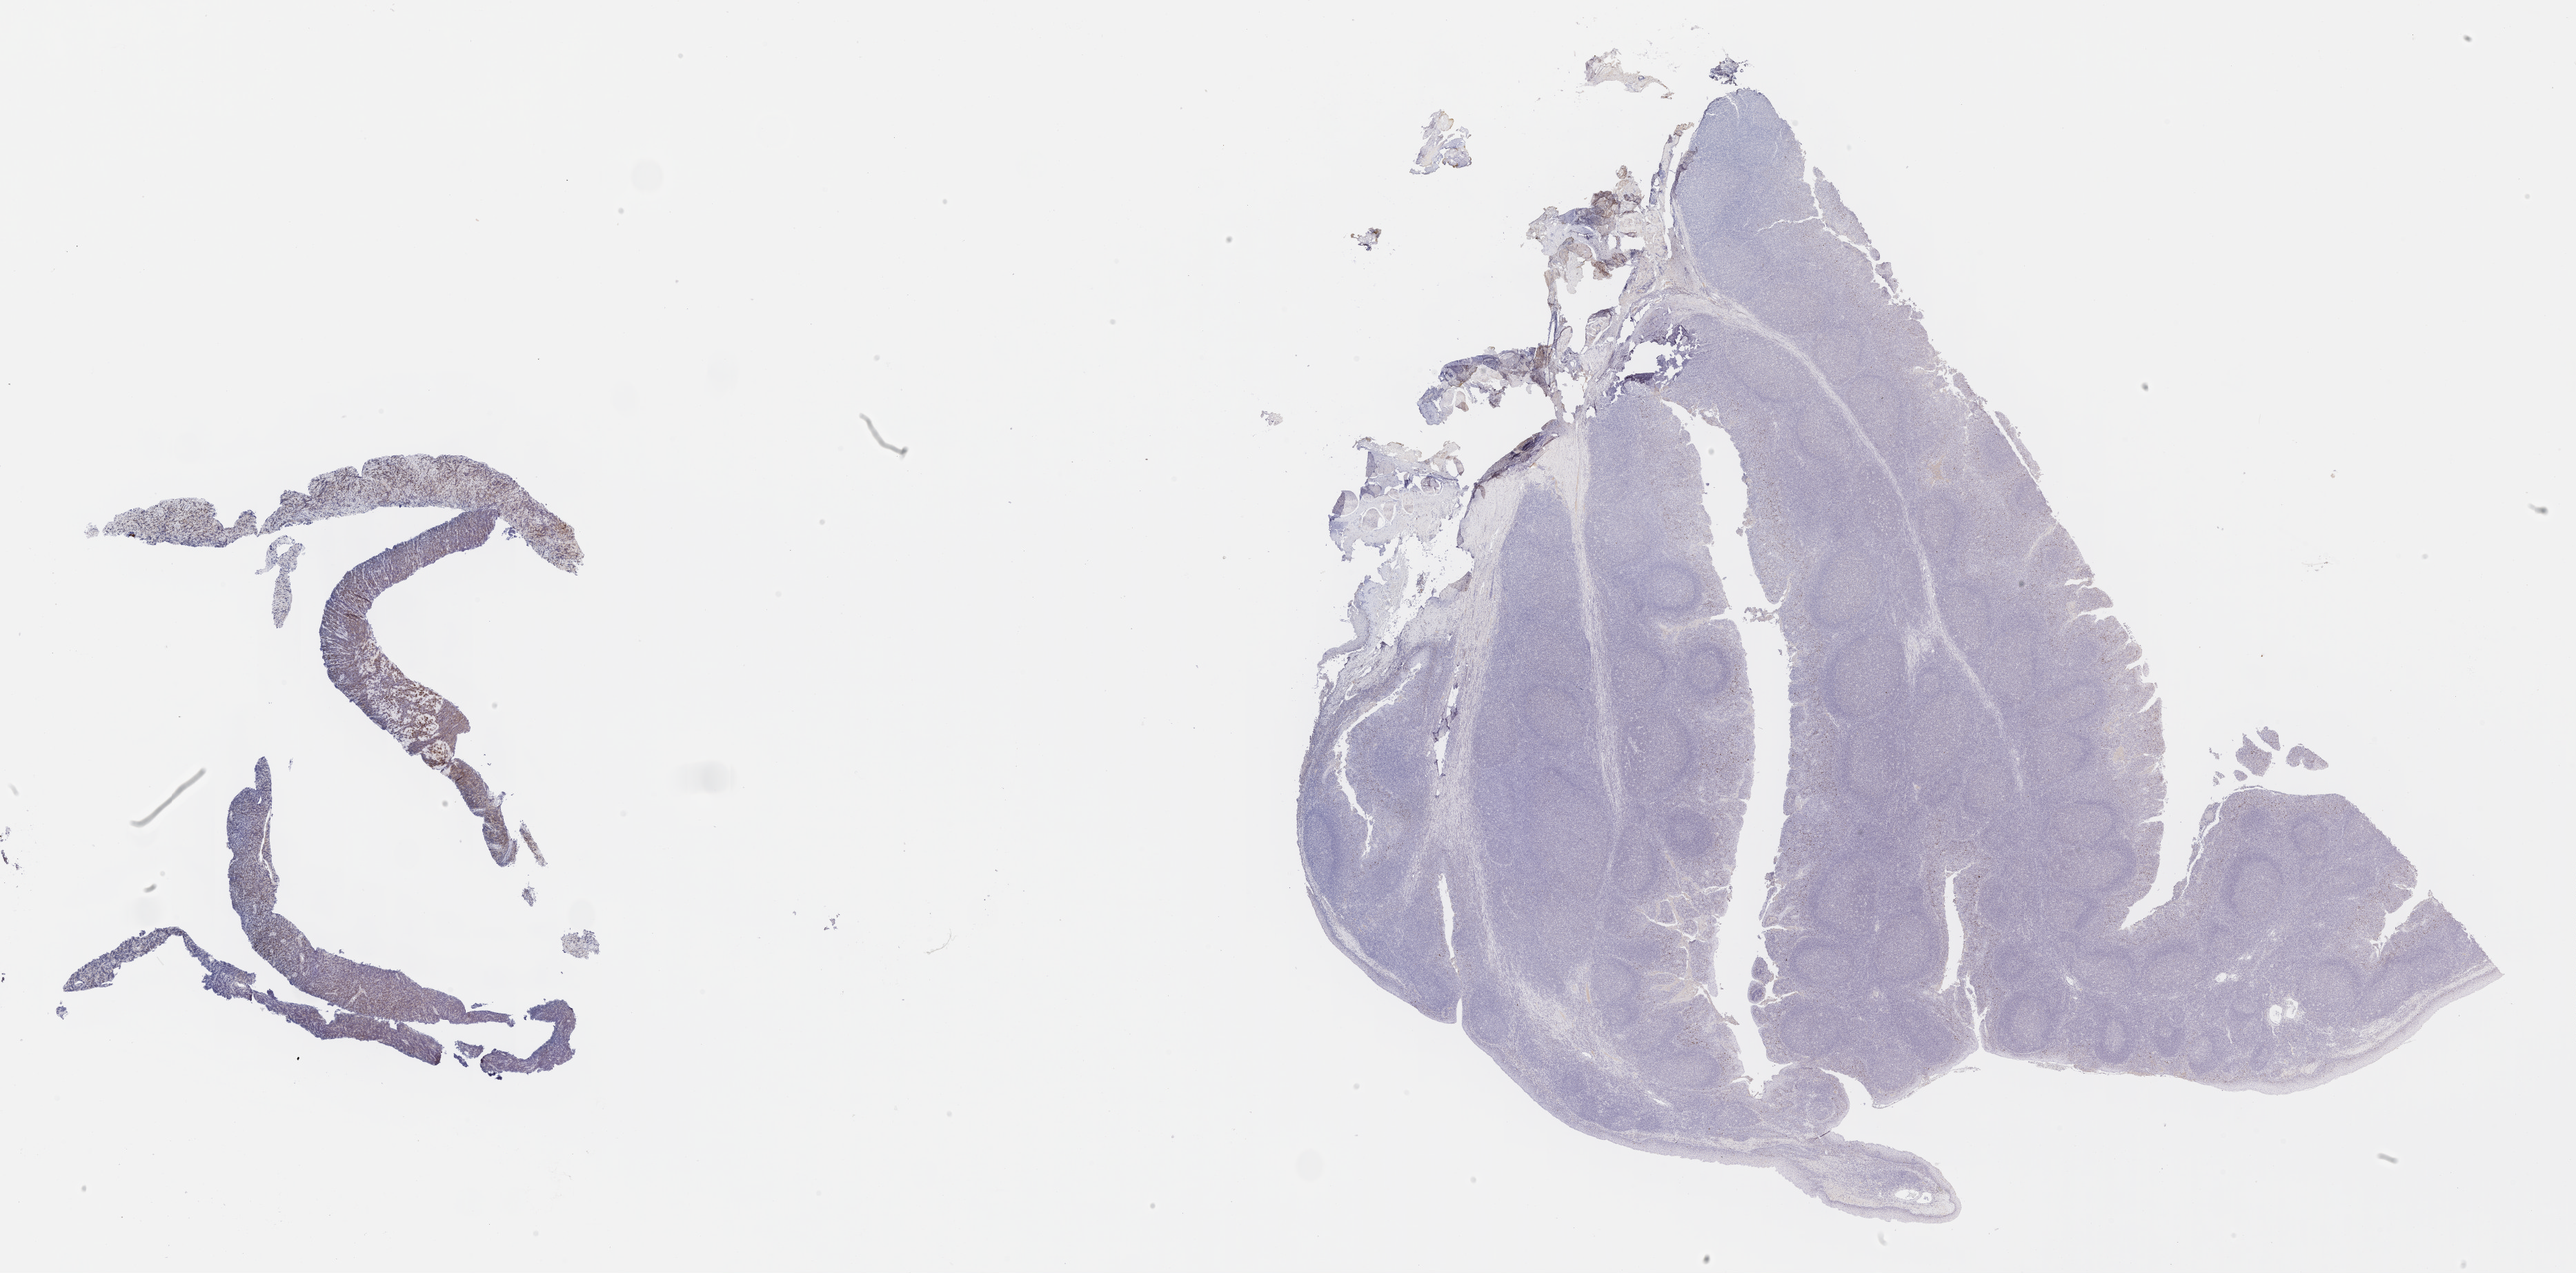
Whole-slide image, immunohistochemical stain for p53, whole scanned area (about 30.2 x 14.9 mm) shown as a low-resolution overview. Tumor tissue. Anatomic site: pleura. Male, age 2 years at initial diagnosis.
Histologic diagnosis: Diffuse large B-cell lymphoma, NOS.